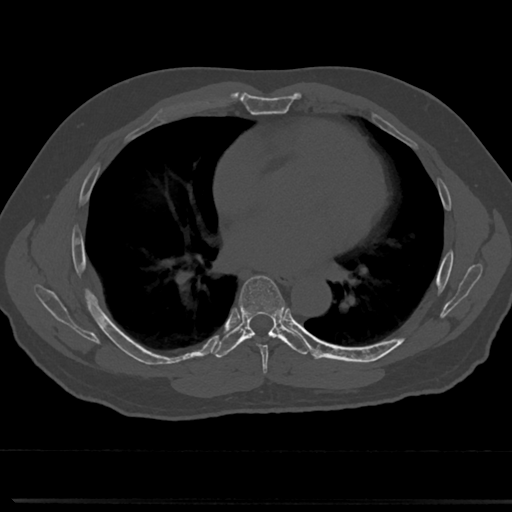
CT including the spine, one axial slice. Slice 420 of 817 in the series (ordered by position). 120 kVp. Bone window (W 1800 / L 400 HU). 0.5 mm slice thickness. 512 × 512 image matrix, field of view 355 × 355 mm. Patient: male, 61 years. From the clinical record (not read from this slice): primary cancer: prostate.
Structures marked on this image (semi-automatic segmentation, software-assisted and operator-edited):
- T6 vertebra: bounding box (x1, y1, x2, y2) in pixels: (240, 275, 287, 361)
- T7 vertebra: (239, 286, 286, 335)